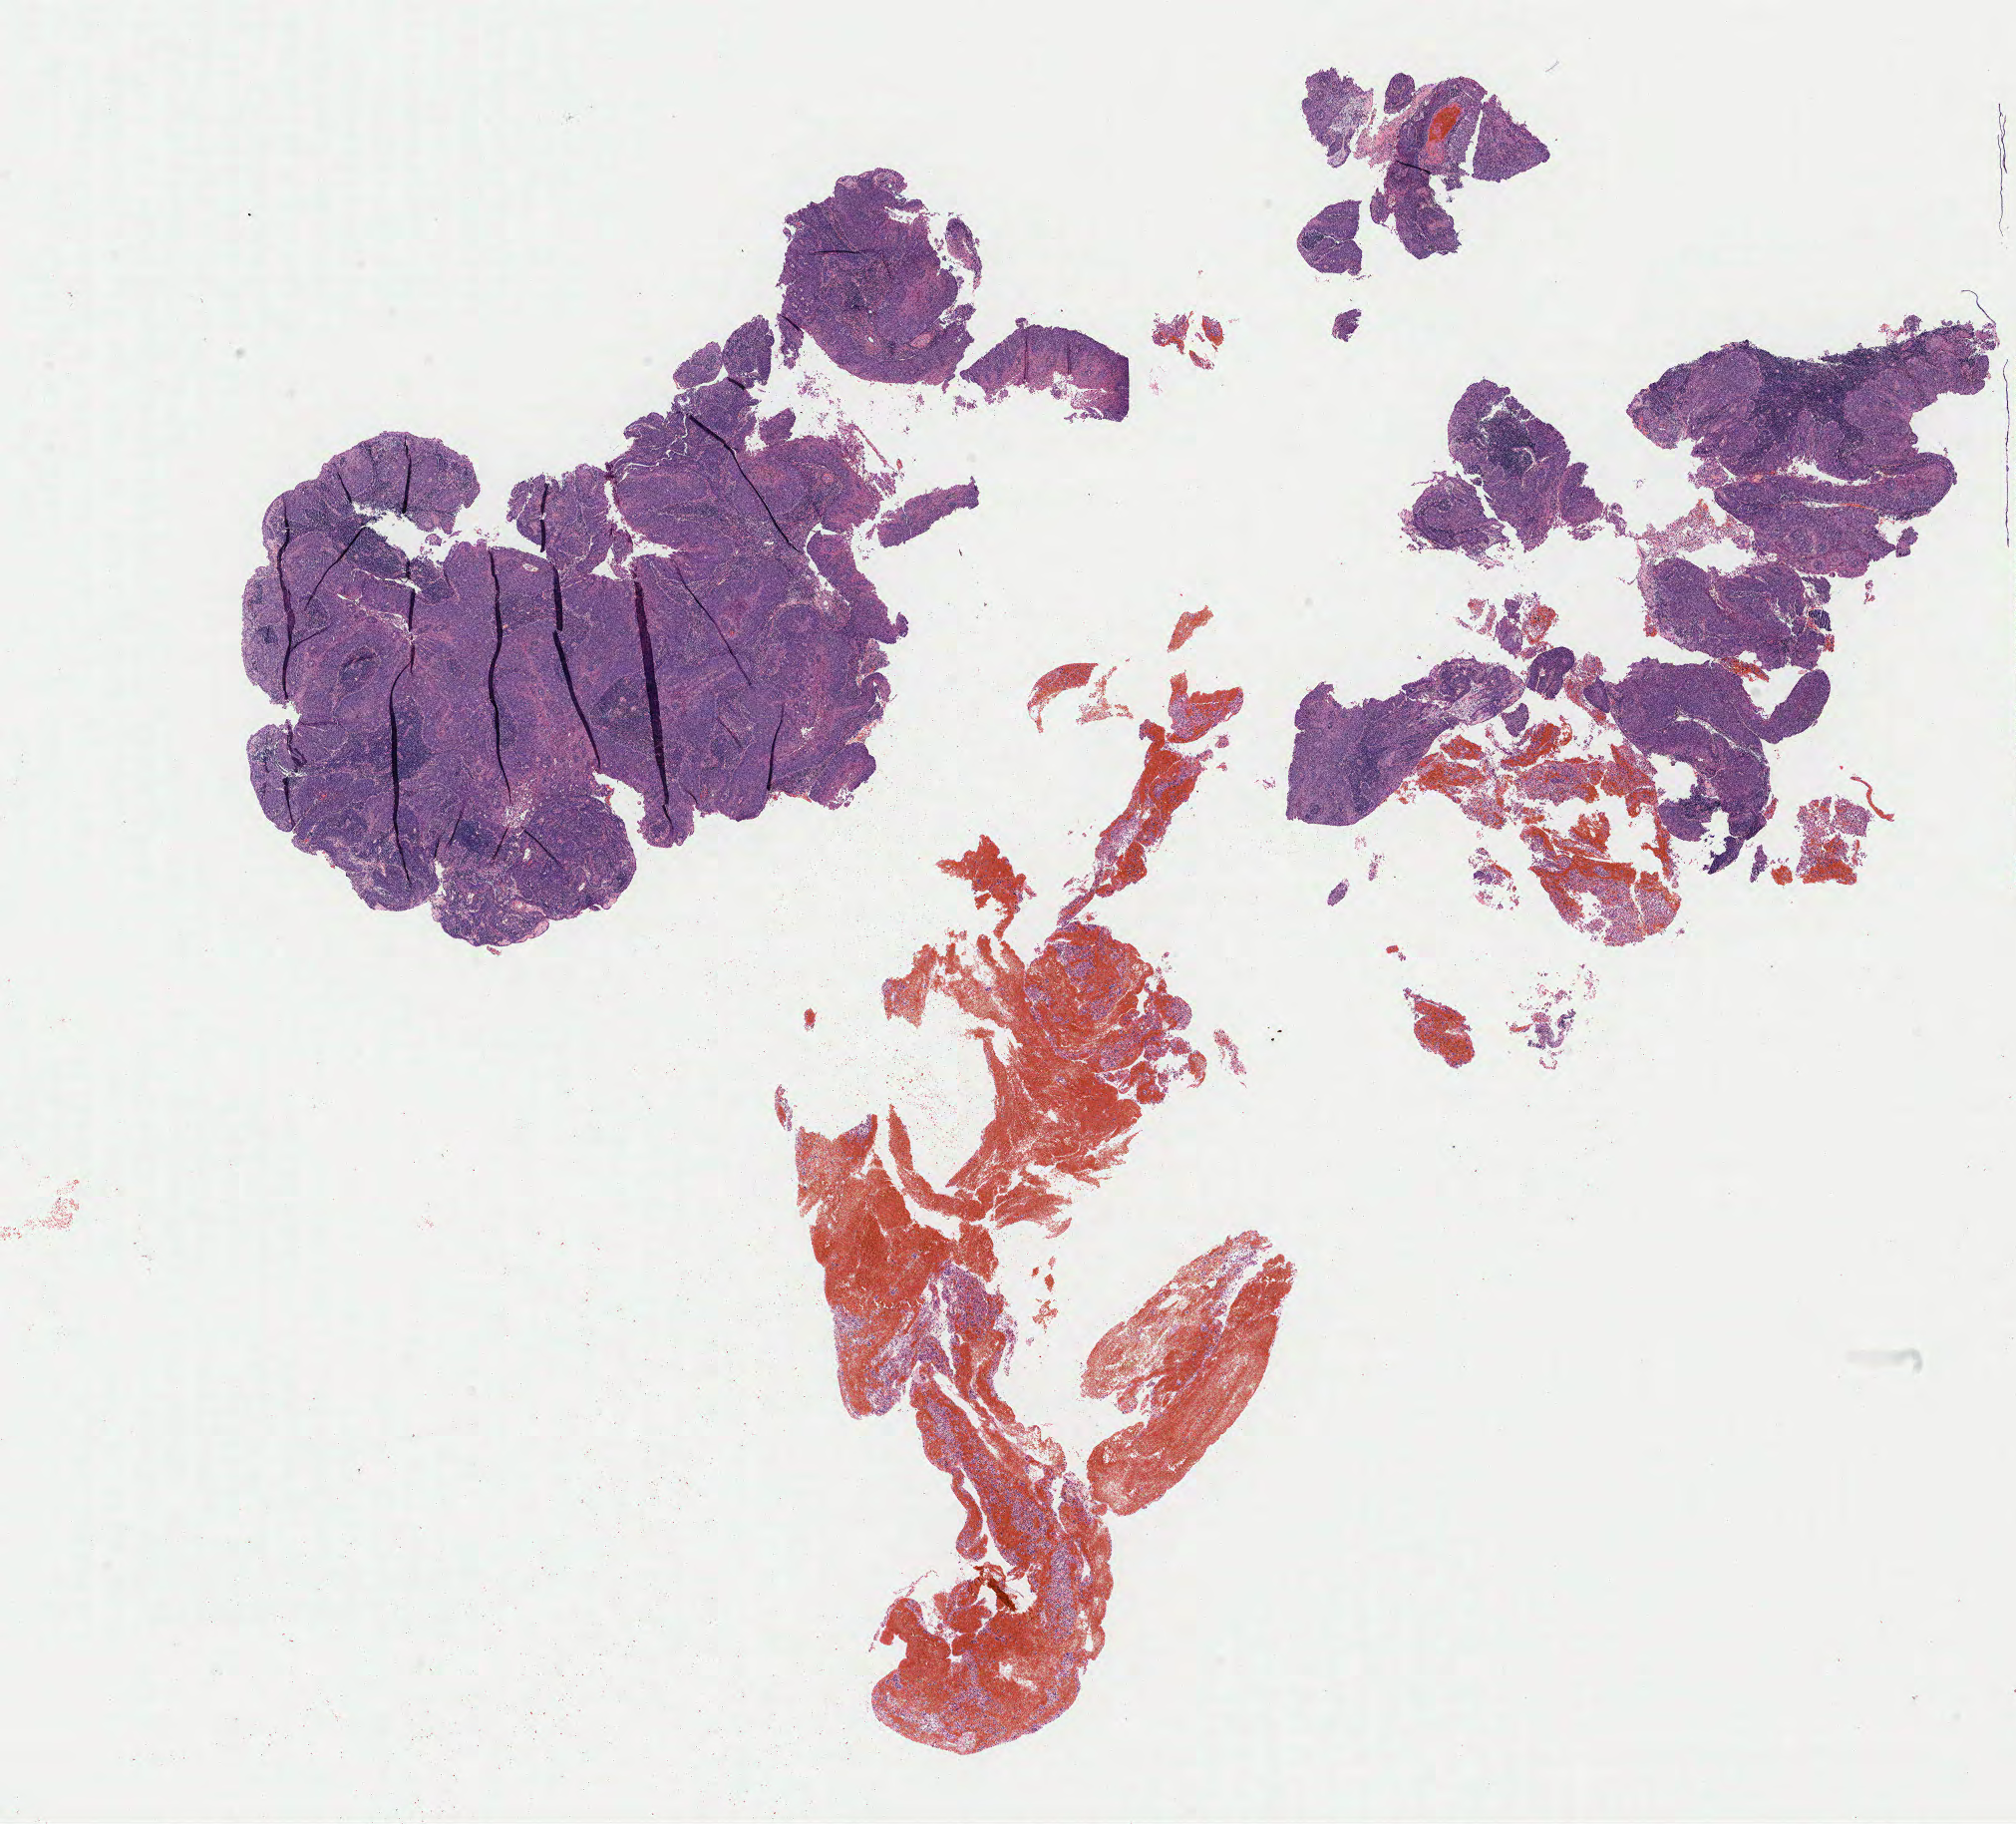
Whole-slide image, H&E stain, shown as a low-resolution overview of the whole scanned area (about 16.1 x 14.5 mm), tumor tissue, site: cervix. Patient: female, age 47 years.
Diagnosis: Squamous cell carcinoma, large cell, nonkeratinizing, NOS.